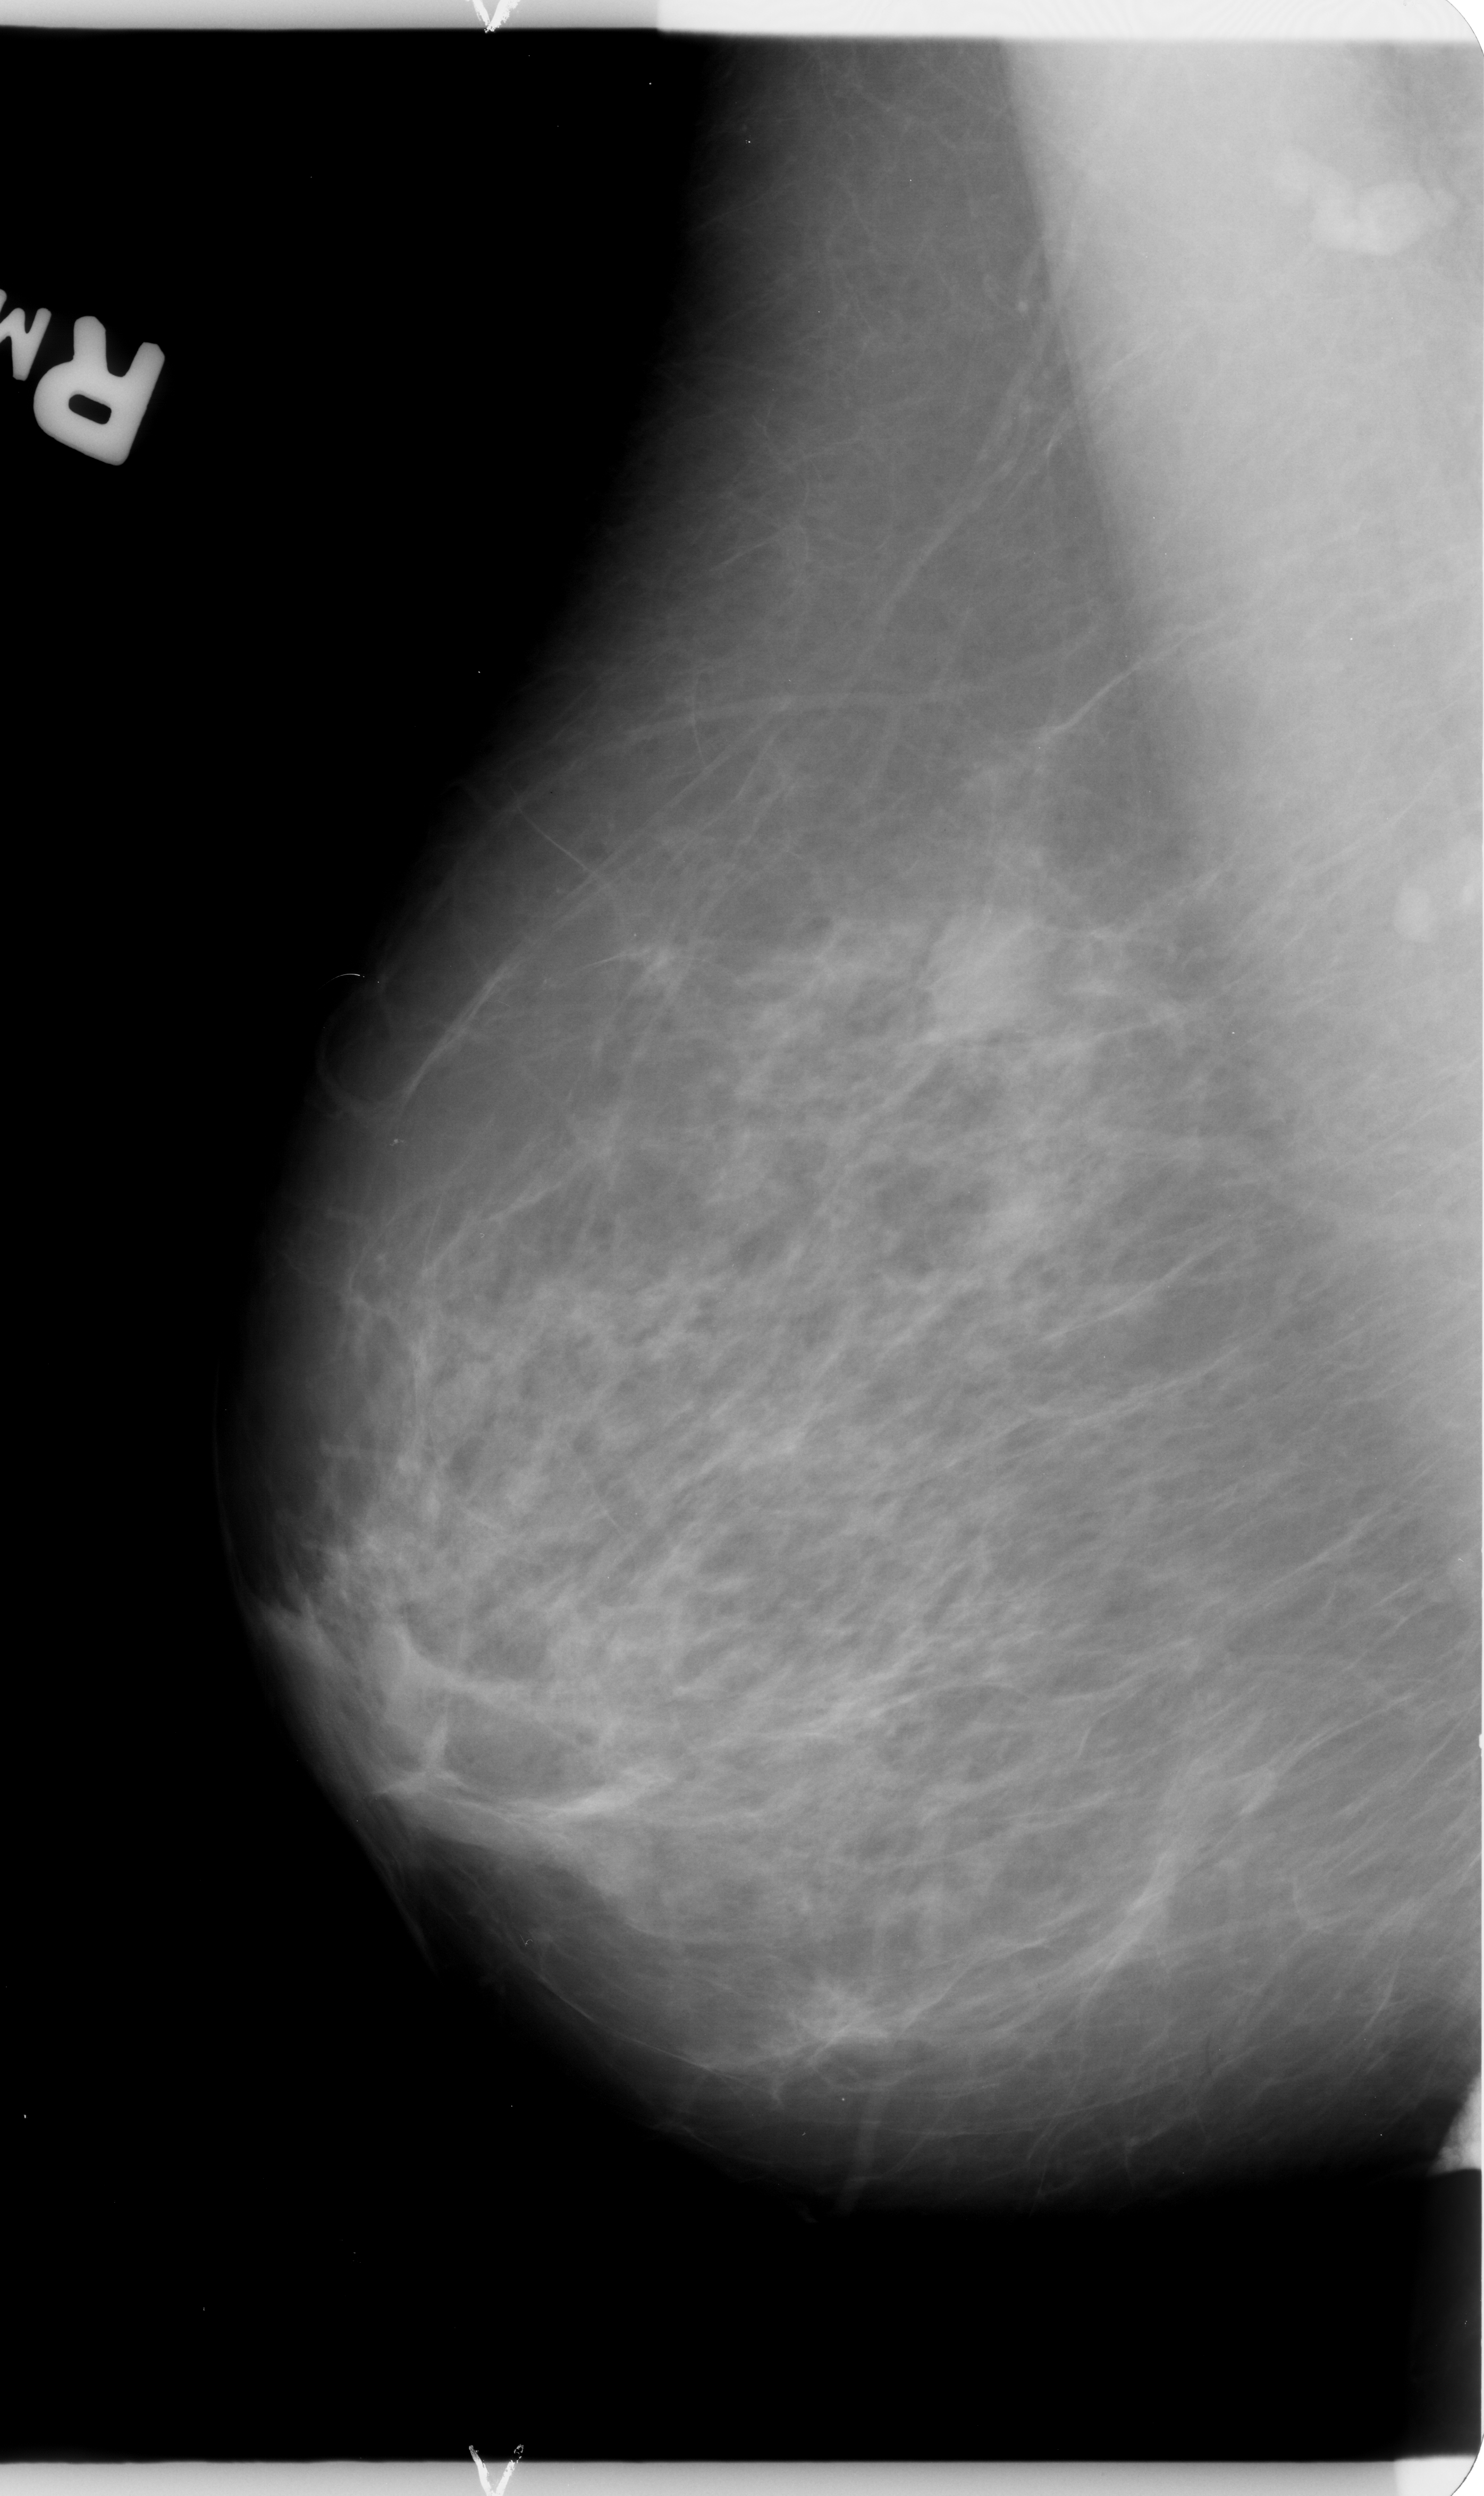
Scanned film-screen mammogram; right breast; mediolateral oblique (MLO) view; BI-RADS breast density category 3 (scale 1–4); 1484 × 2496 image matrix.
Expert-marked regions of interest on this image (one box per marked abnormality):
- mass, shape round, margins circumscribed / ill defined; BI-RADS assessment category 4; pathology (as recorded): benign: bounding box [x1, y1, x2, y2] px = [916, 894, 1050, 1042]